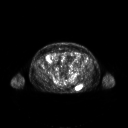
FDG PET of an extremity soft-tissue mass (from a PET/CT study), one axial slice; slice 81 of 267 in the series (ordered by position); 3.27 mm slice thickness; 128 × 128 image matrix. Patient: male, 61 years. Case-level facts recorded for this patient, not image findings: histological type: pleiomorphic leiomyosarcoma; grade: high; site of the primary tumour: left buttock.
Annotated regions visible in this slice (expert contour drawn on MRI and transferred to this co-registered scan by the dataset authors):
- gross tumour volume including surrounding oedema: bounding box (x1, y1, x2, y2) in pixels: (79, 85, 82, 89)
- gross tumour volume (mass): (79, 86, 81, 89)